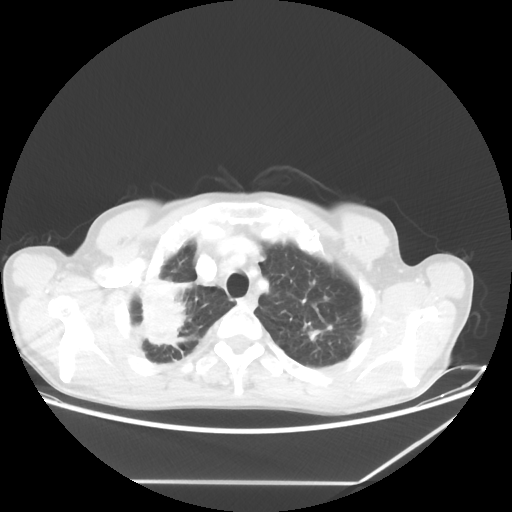
Chest CT, one axial slice; slice 55 of 65 in the series (ordered by position); 80 kVp; lung window (W 1500 / L -600 HU); 512 × 512 image matrix, field of view 397 × 397 mm. Patient: male, 68 years. From the clinical record (not read from this slice): clinical TNM (as recorded): T3 N3 M0.
Annotated regions visible in this slice (bounding box drawn by a radiologist):
- lung tumour (recorded histology: adenocarcinoma): bounding box [x1, y1, x2, y2] px = [125, 265, 194, 356]